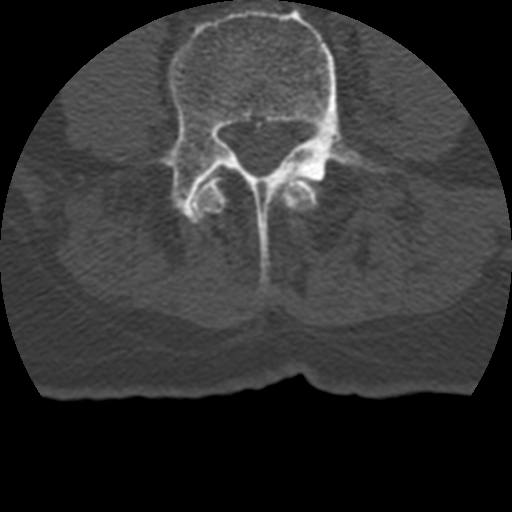
CT including the spine, one axial slice; slice 69 of 399 in the series (ordered by position); 120 kVp; bone window (W 1800 / L 400 HU); 512 × 512 image matrix, field of view 160 × 160 mm. Patient age 69 years. From the clinical record (not read from this slice): primary cancer: prostate.
Outlined on this slice (semi-automatic segmentation, software-assisted and operator-edited):
- L3 vertebra: bounding box (x1, y1, x2, y2) in pixels: (196, 177, 318, 214)
- L4 vertebra: (157, 8, 374, 280)